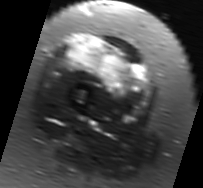
MRI of an extremity soft-tissue mass, one axial slice; slice 23 of 91 in the series (ordered by position); T2-weighted fat-saturated; MR volume resampled by the dataset authors to the PET/CT grid (not the native acquisition matrix); 203 × 188 image matrix, field of view 198 × 184 mm. Female patient. Case-level facts recorded for this patient, not image findings: histological type: malignant solitary fibrous tumor; grade: intermediate; site of the primary tumour: right thigh.
Structures marked on this image (expert contour drawn on MRI and transferred to this co-registered scan by the dataset authors):
- gross tumour volume including surrounding oedema: bounding box (x1, y1, x2, y2) in pixels: (67, 35, 153, 102)
- gross tumour volume (mass): (99, 56, 125, 82)